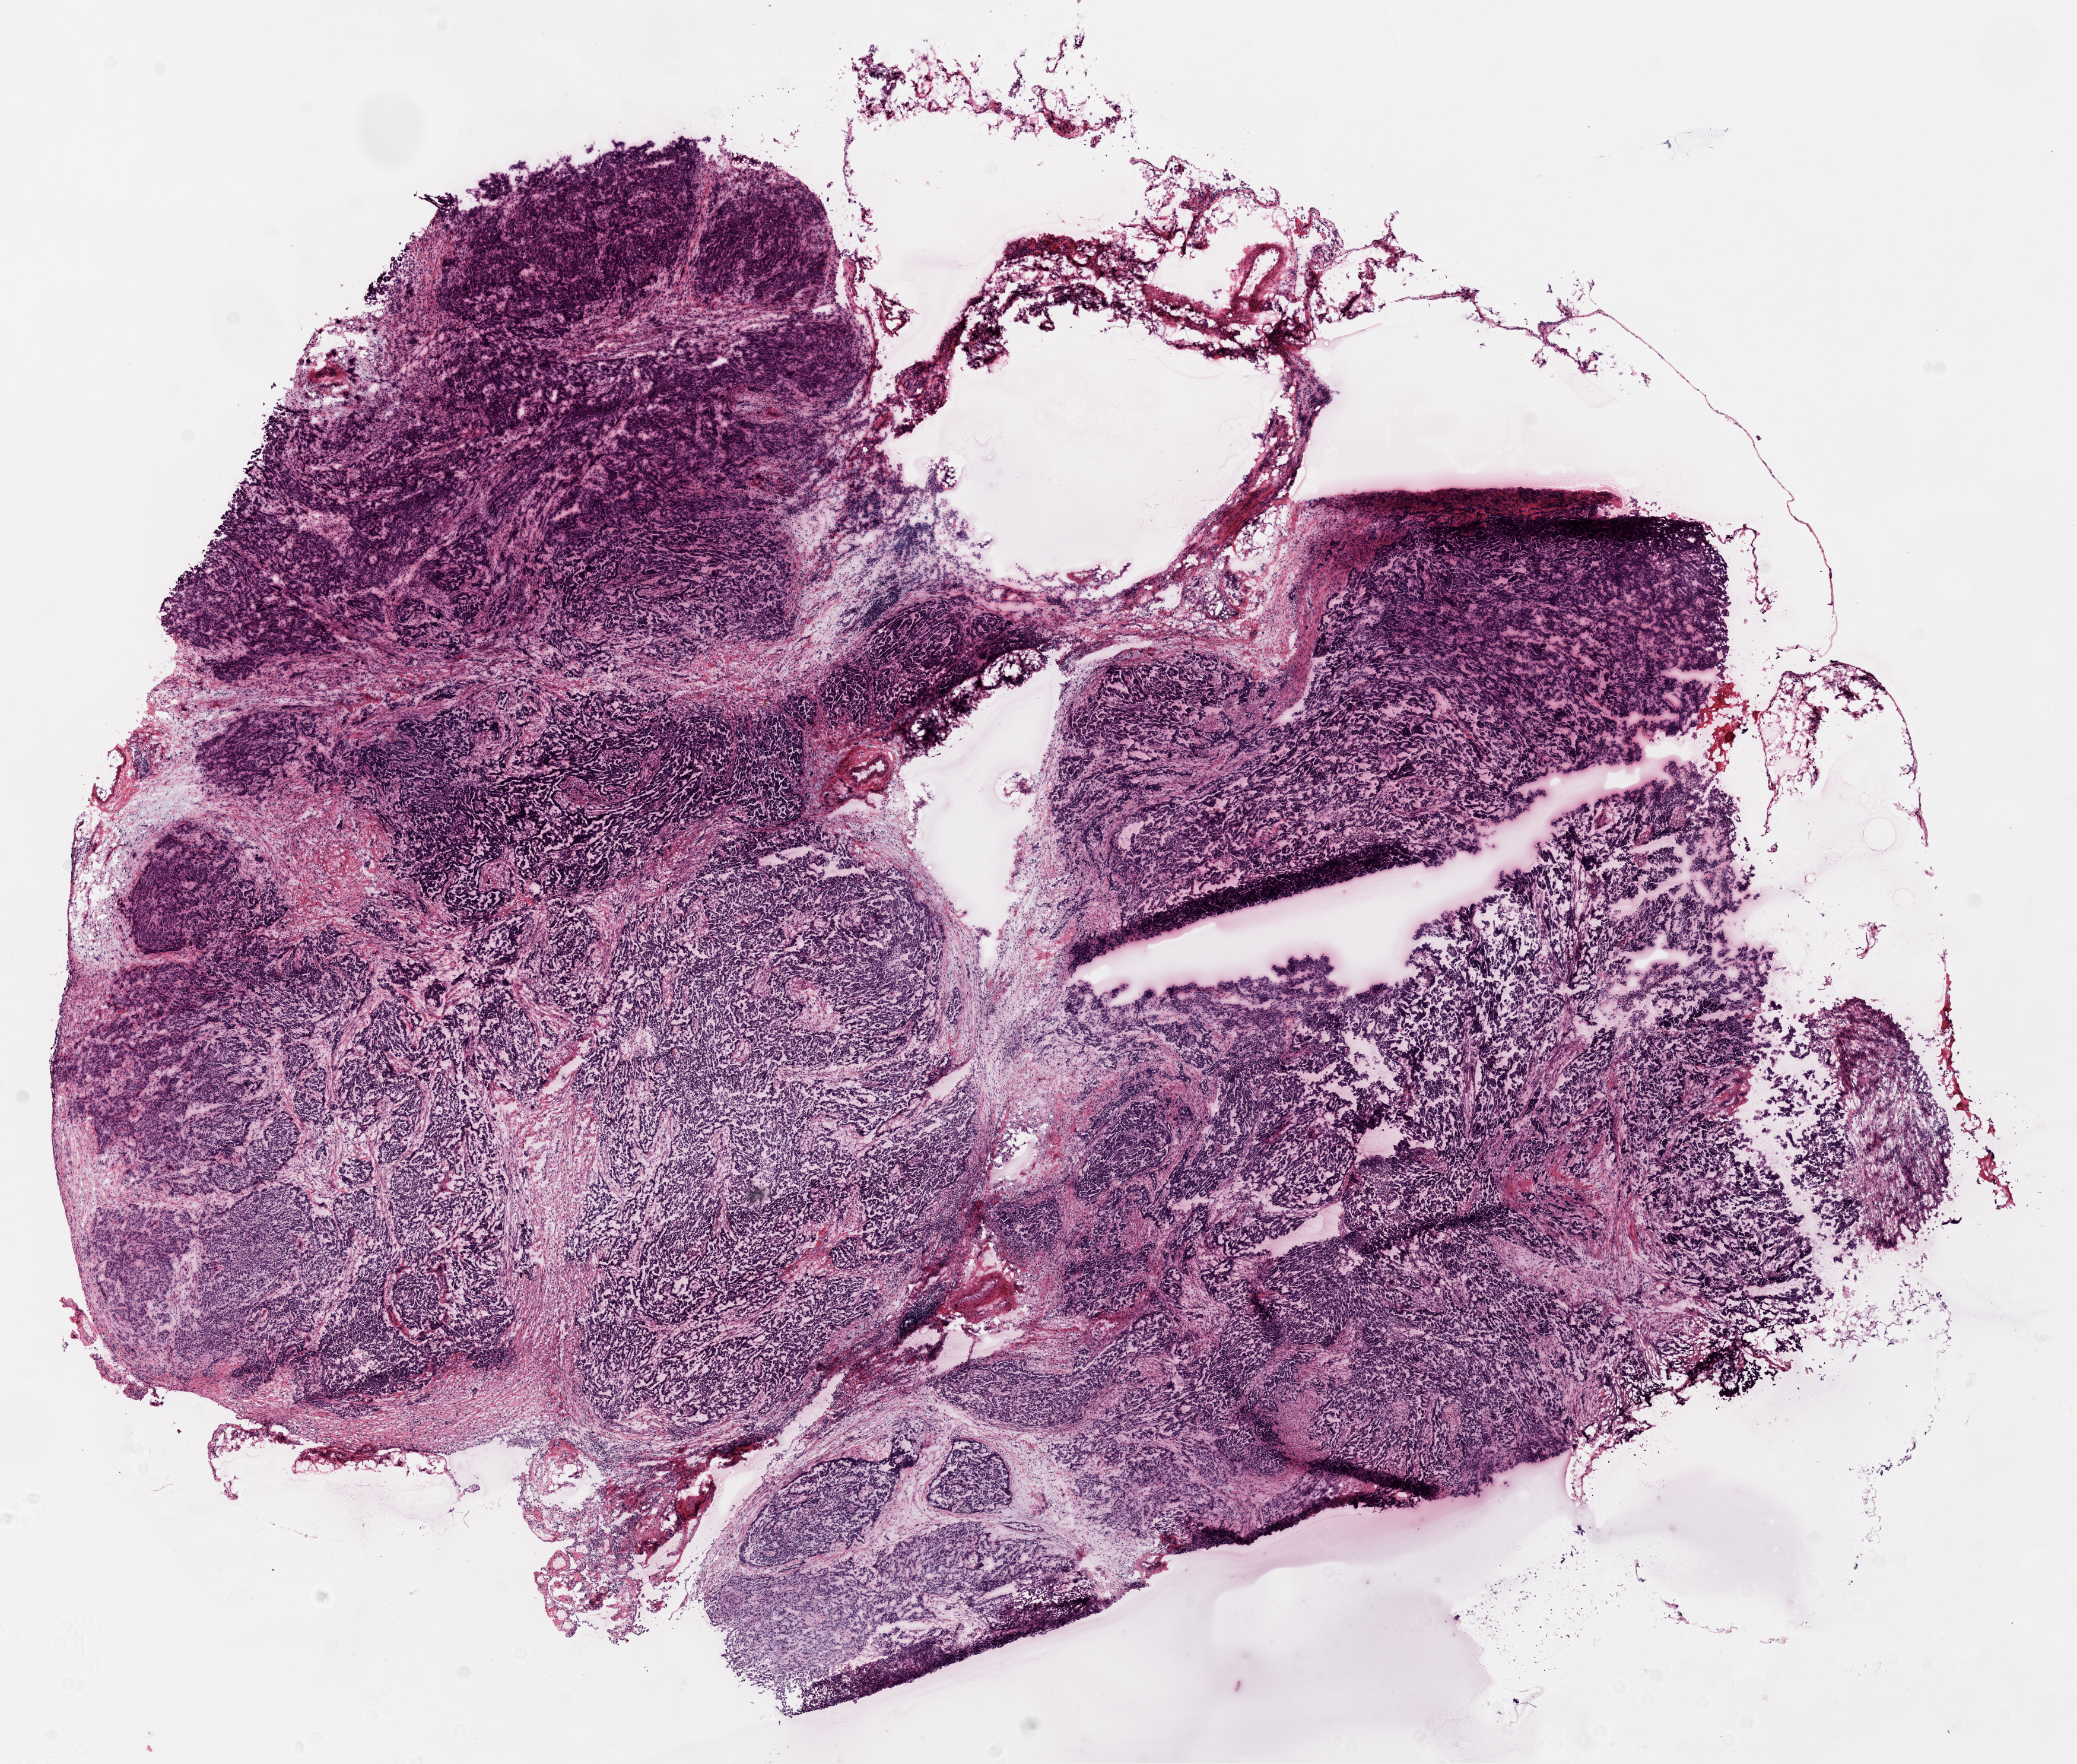
Whole-slide histology image, H&E-stained, a low-resolution overview of the entire scanned area, about 14.0 x 11.9 mm (acquisition: 20x scan); frozen section from the top of the tissue portion; primary tumour sample from the ovary. Female patient; age at initial diagnosis 58 years. Histologic grade: G3 (poorly differentiated). Slide review estimates, as recorded: tumour cells 90%, tumour nuclei 90%, normal cells 0%, stromal cells 10%, necrosis 0%.
* FIGO stage: IV
* laterality: bilateral
* histologic diagnosis: Serous cystadenocarcinoma, NOS